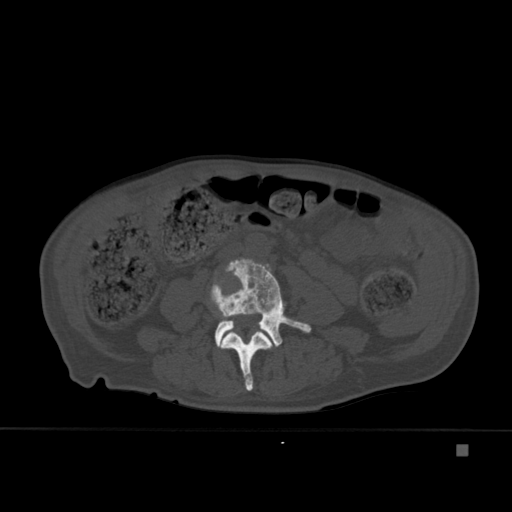
CT including the spine, one axial slice; slice 132 of 451 in the series (ordered by position); bone window (W 1800 / L 400 HU); 1.5 mm slice thickness; 512 × 512 image matrix, field of view 378 × 378 mm. Patient: male, 75 years. Case-level facts recorded for this patient, not image findings: primary cancer: prostate.
Outlined on this slice (semi-automatically segmented with operator editing):
- L3 vertebra: bounding box (x1, y1, x2, y2) in pixels: (220, 331, 273, 391)
- L4 vertebra: (210, 258, 312, 347)